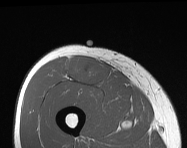
MRI of an extremity soft-tissue mass, one axial slice; position 59 of 114 along the scan axis; MR volume resampled by the dataset authors to the PET/CT grid (not the native acquisition matrix); 3.27 mm slice thickness; 187 × 148 image matrix, field of view 183 × 145 mm. Male patient. From the clinical record (not read from this slice): histological type: pleiomorphic leiomyosarcoma; grade: intermediate; site of the primary tumour: right thigh.
Annotated regions visible in this slice (expert contour drawn on MRI and transferred to this co-registered scan by the dataset authors):
- gross tumour volume including surrounding oedema: box from (x=68, y=56) to (x=113, y=87) px